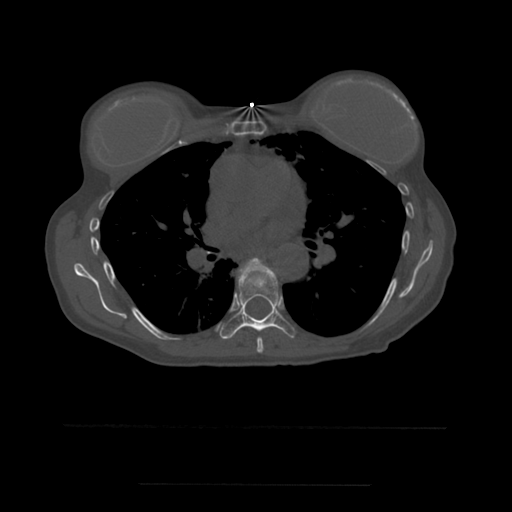
CT including the spine, one axial slice. Bone window (W 1800 / L 400 HU). 1.25 mm slice thickness. 512 × 512 image matrix. Patient age 58 years. Case-level facts recorded for this patient, not image findings: primary cancer: lung.
Outlined on this slice (semi-automatically segmented with operator editing):
- T6 vertebra: bounding box (x1, y1, x2, y2) in pixels: (257, 338, 264, 354)
- T7 vertebra: (216, 258, 295, 339)